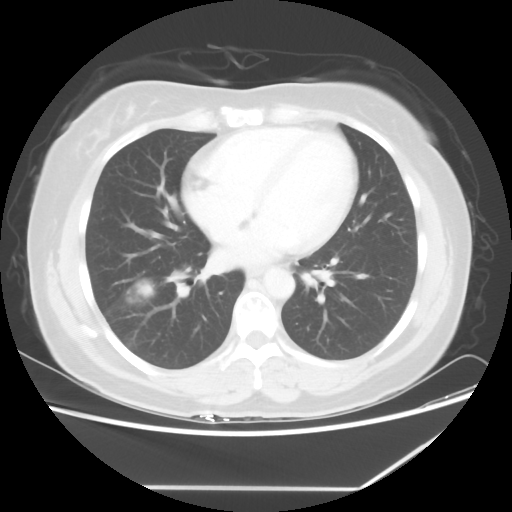
Chest CT, one axial slice; position 27 of 60 along the scan axis; 100 kVp; lung window (W 1500 / L -600 HU); 5 mm slice thickness; 512 × 512 image matrix, field of view 374 × 374 mm. Female patient, age 42 years. From the clinical record (not read from this slice): clinical TNM (as recorded): T2 N1 M0.
Structures marked on this image (rectangle marked by the reading radiologist):
- lung tumour (recorded histology: adenocarcinoma): bounding box [x1, y1, x2, y2] px = [137, 278, 150, 298]